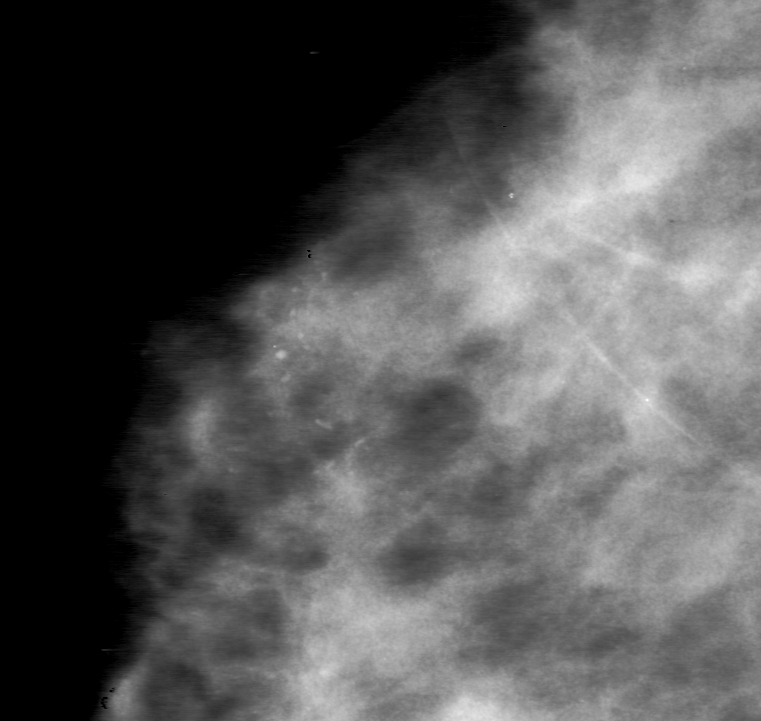
Region of interest cut from a scanned film mammogram (one marked finding), right breast, CC view, BI-RADS breast density category 3 (scale 1–4).
- Finding: calcifications, morphology punctate / fine linear branching, distribution clustered; BI-RADS assessment category 0; subtlety rating 5 on a 1 (subtle) to 5 (obvious) scale; pathology result (as recorded, not read from the image): malignant.